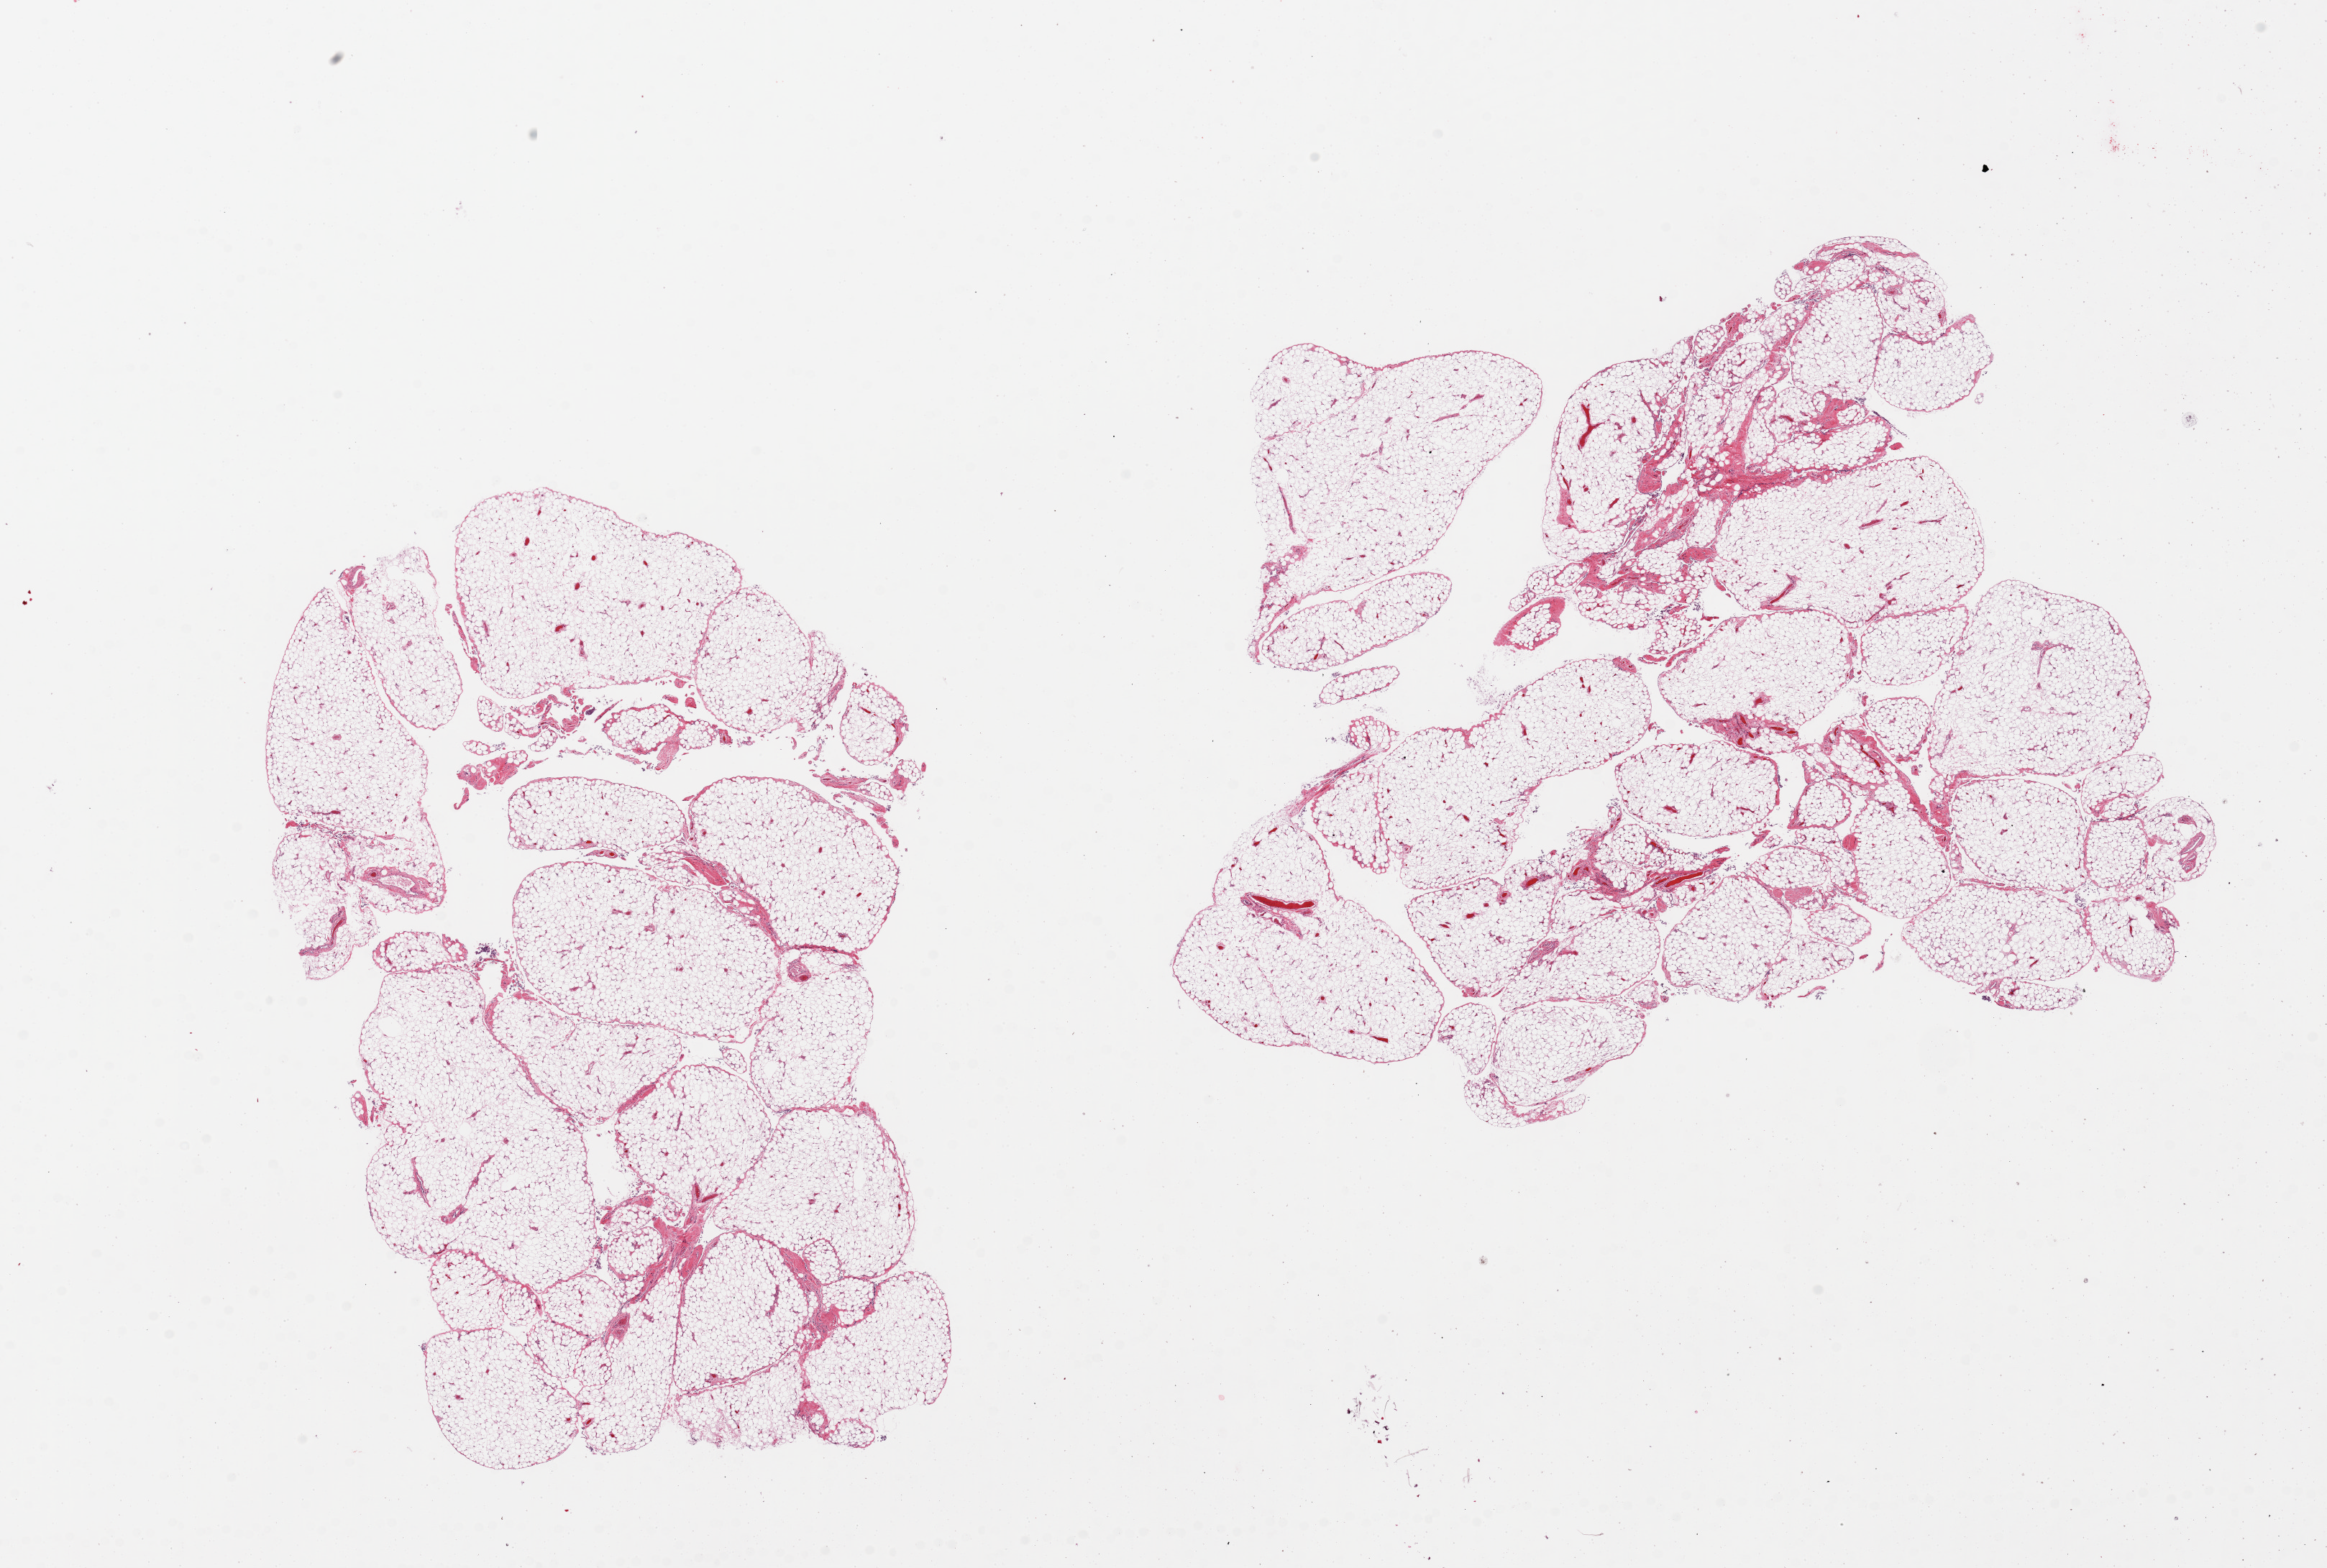
Digitized H&E-stained section, brightfield, shown as a low-resolution overview of the whole scanned area (about 25.6 x 17.3 mm, from a 20x scan). PAXgene-fixed, paraffin-embedded tissue. Target tissue: omentum. Donor tissue sample.
Review note (as recorded): 2 pieces.